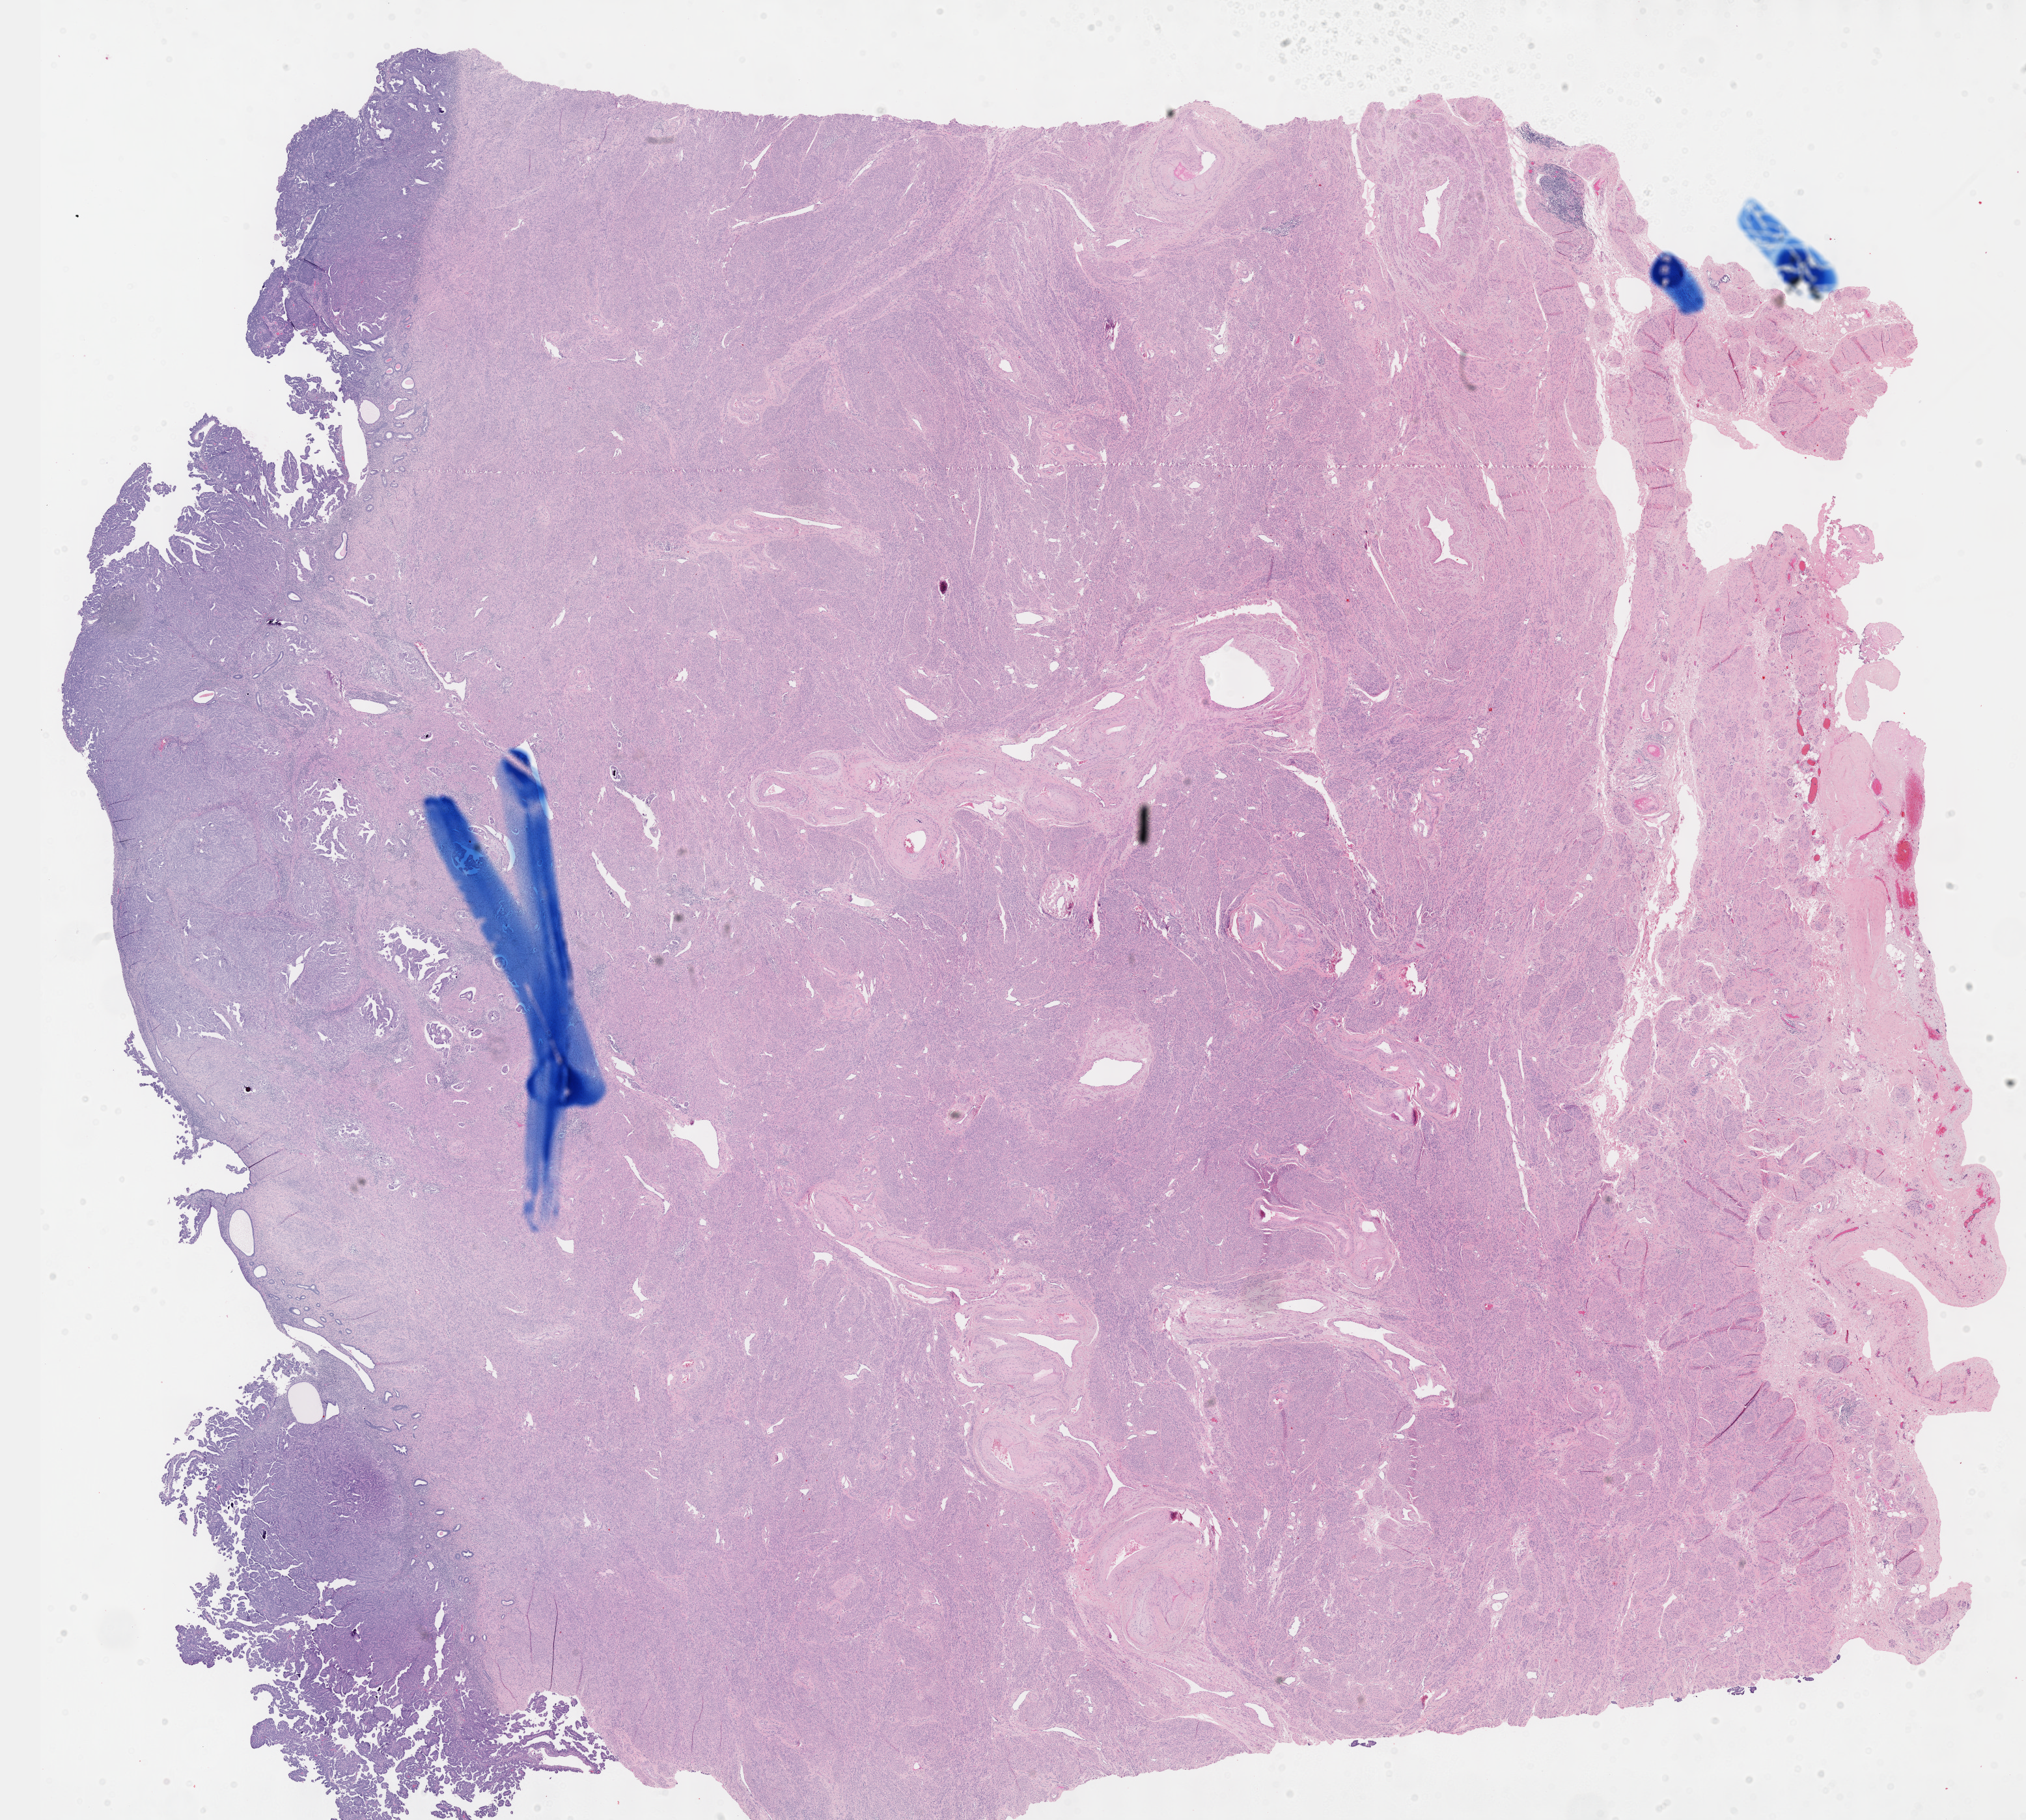
Whole-slide histology image, H&E-stained — whole scanned area (about 25.1 x 22.6 mm, acquisition: 40x scan) shown as a low-resolution overview, formalin-fixed paraffin-embedded (FFPE) diagnostic section, primary tumour sample from the uterus. Female, age 73 years at initial diagnosis. Histologic grade: G3 (poorly differentiated).
Pathologic diagnosis: Serous surface papillary carcinoma. FIGO stage: IA.